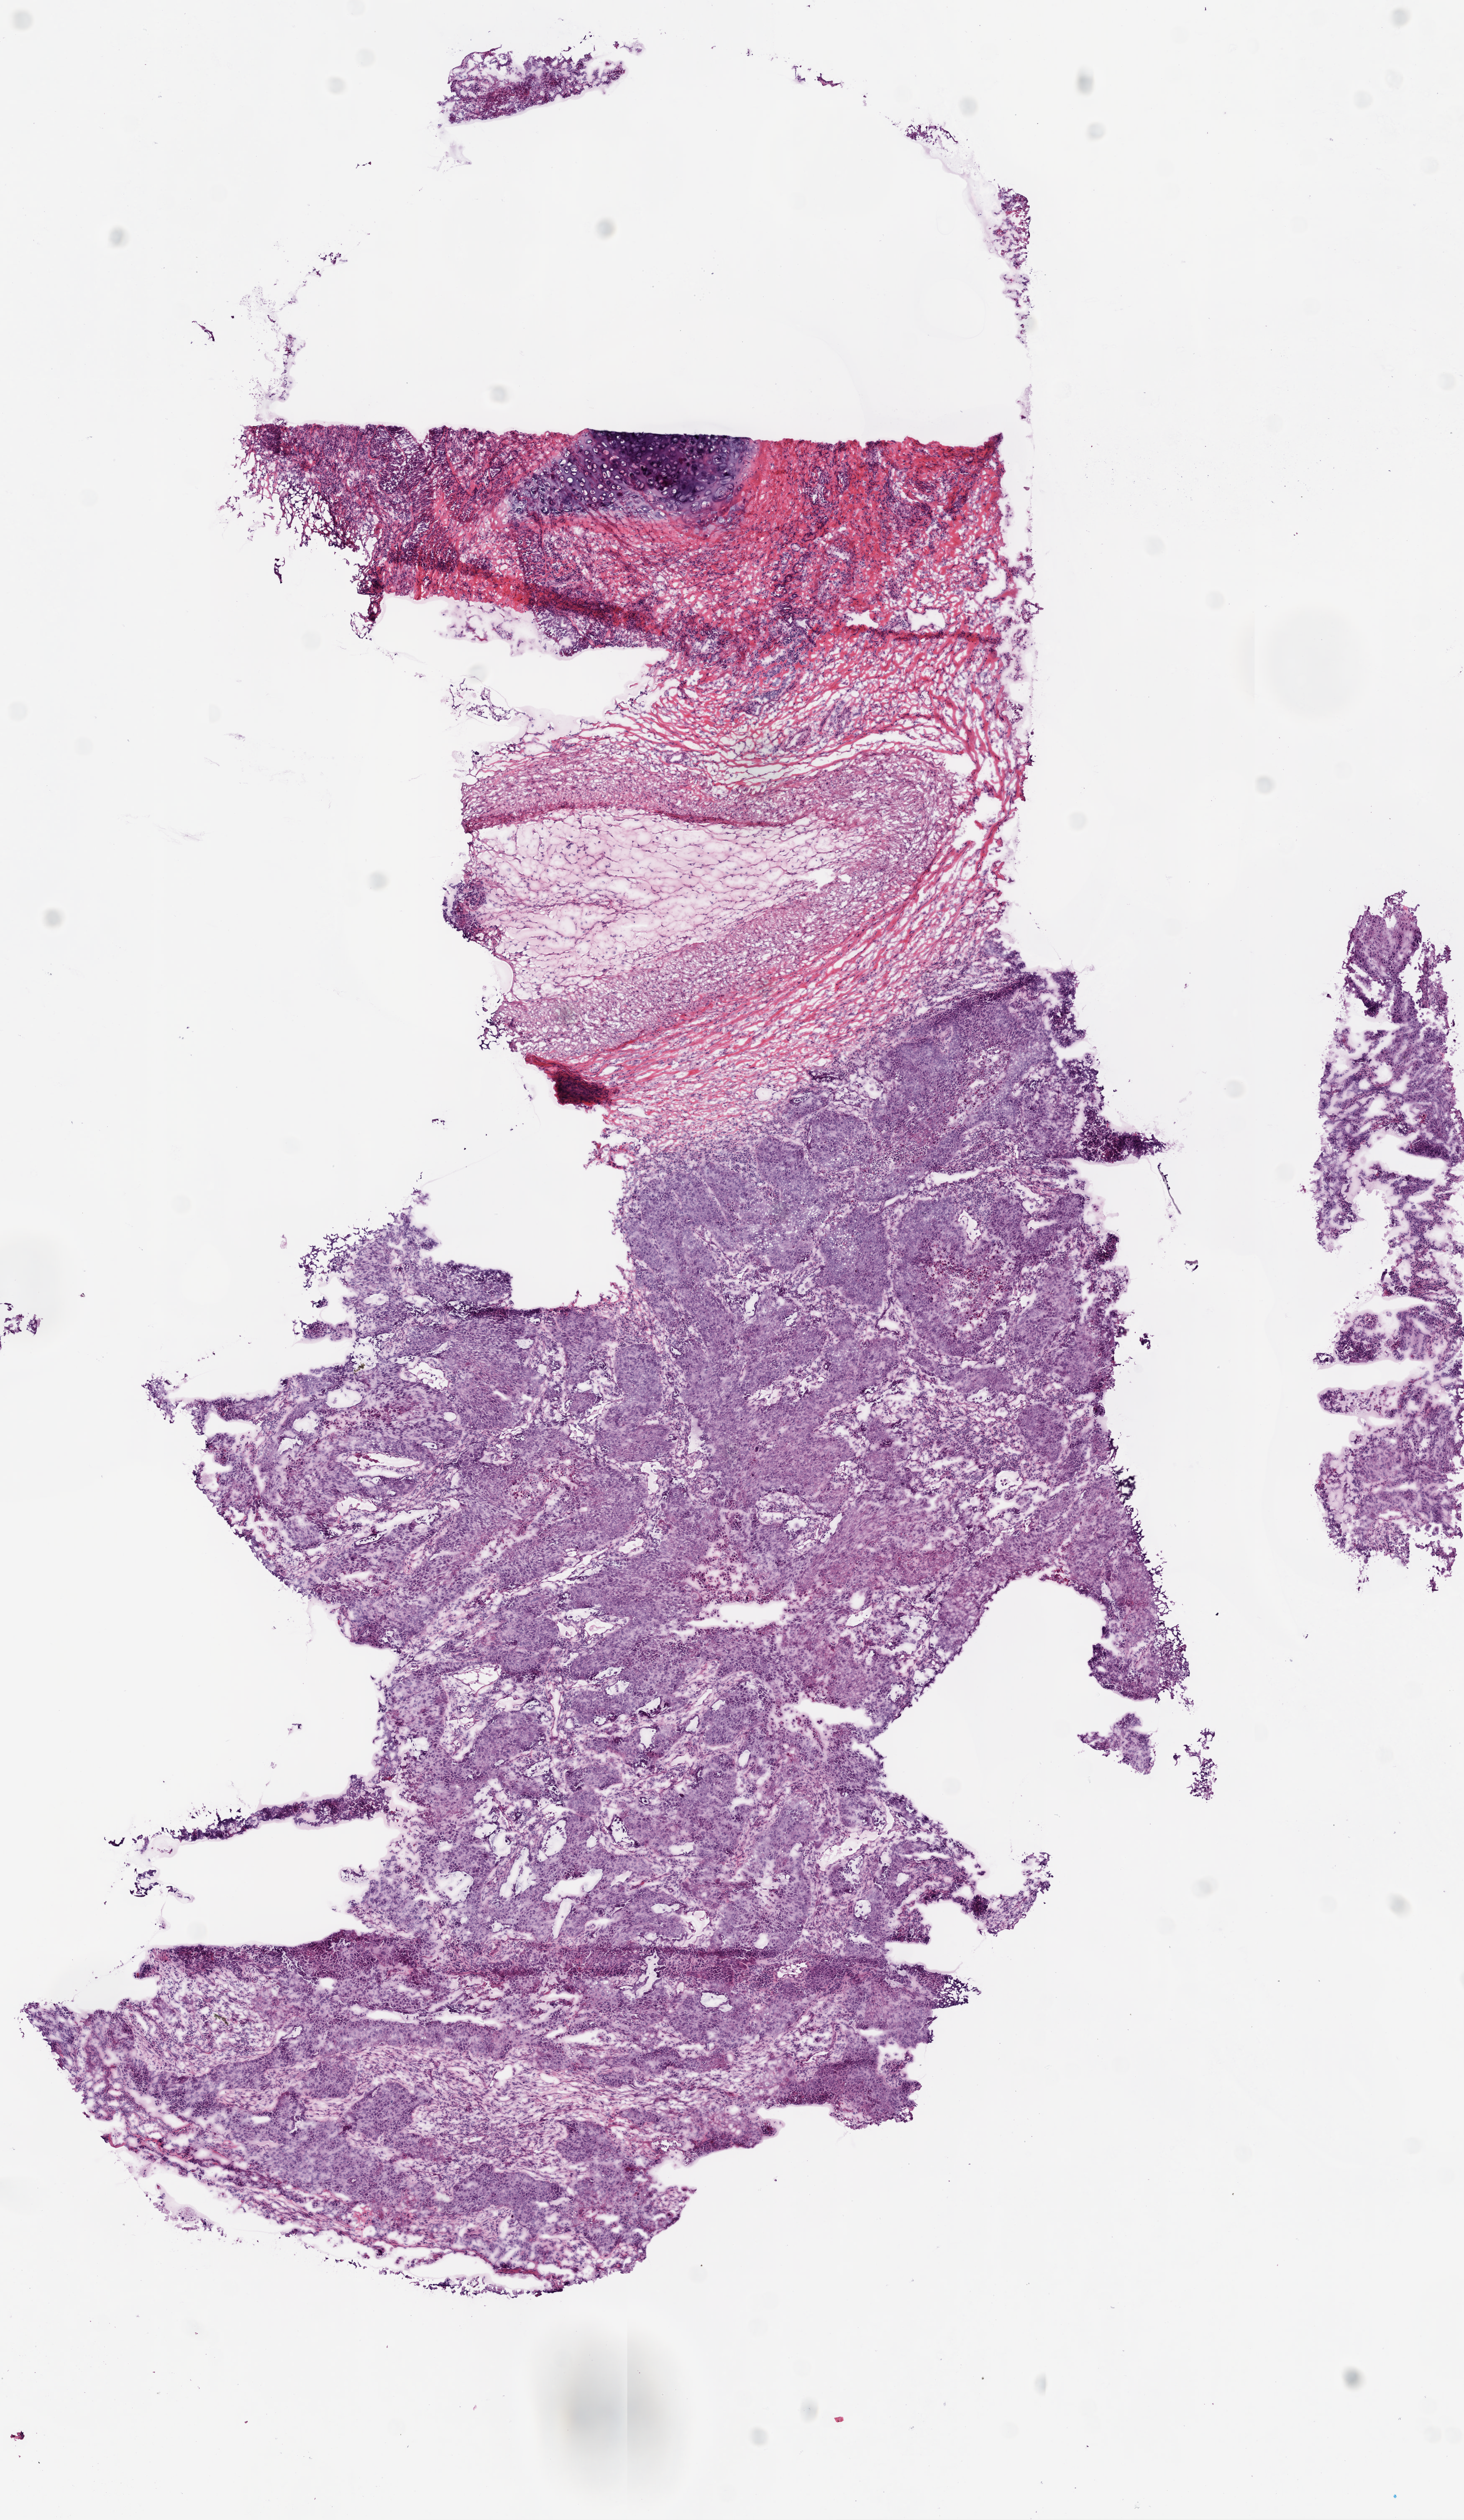
Digitized Hematoxylin and eosin (H&E) stained tissue section (whole slide) — a low-resolution overview of the entire scanned area, about 7.0 x 12.1 mm (acquisition: 20x scan). Frozen section. Lung, primary tumour sample. Patient: male, age at initial diagnosis 65 years. Slide review estimates, as recorded: tumour cells 50%, tumour nuclei 80%, normal cells 40%, stromal cells 5%, necrosis 5%.
* pathologic diagnosis: Squamous cell carcinoma, NOS (lower lobe, lung)
* AJCC pathologic stage: IB